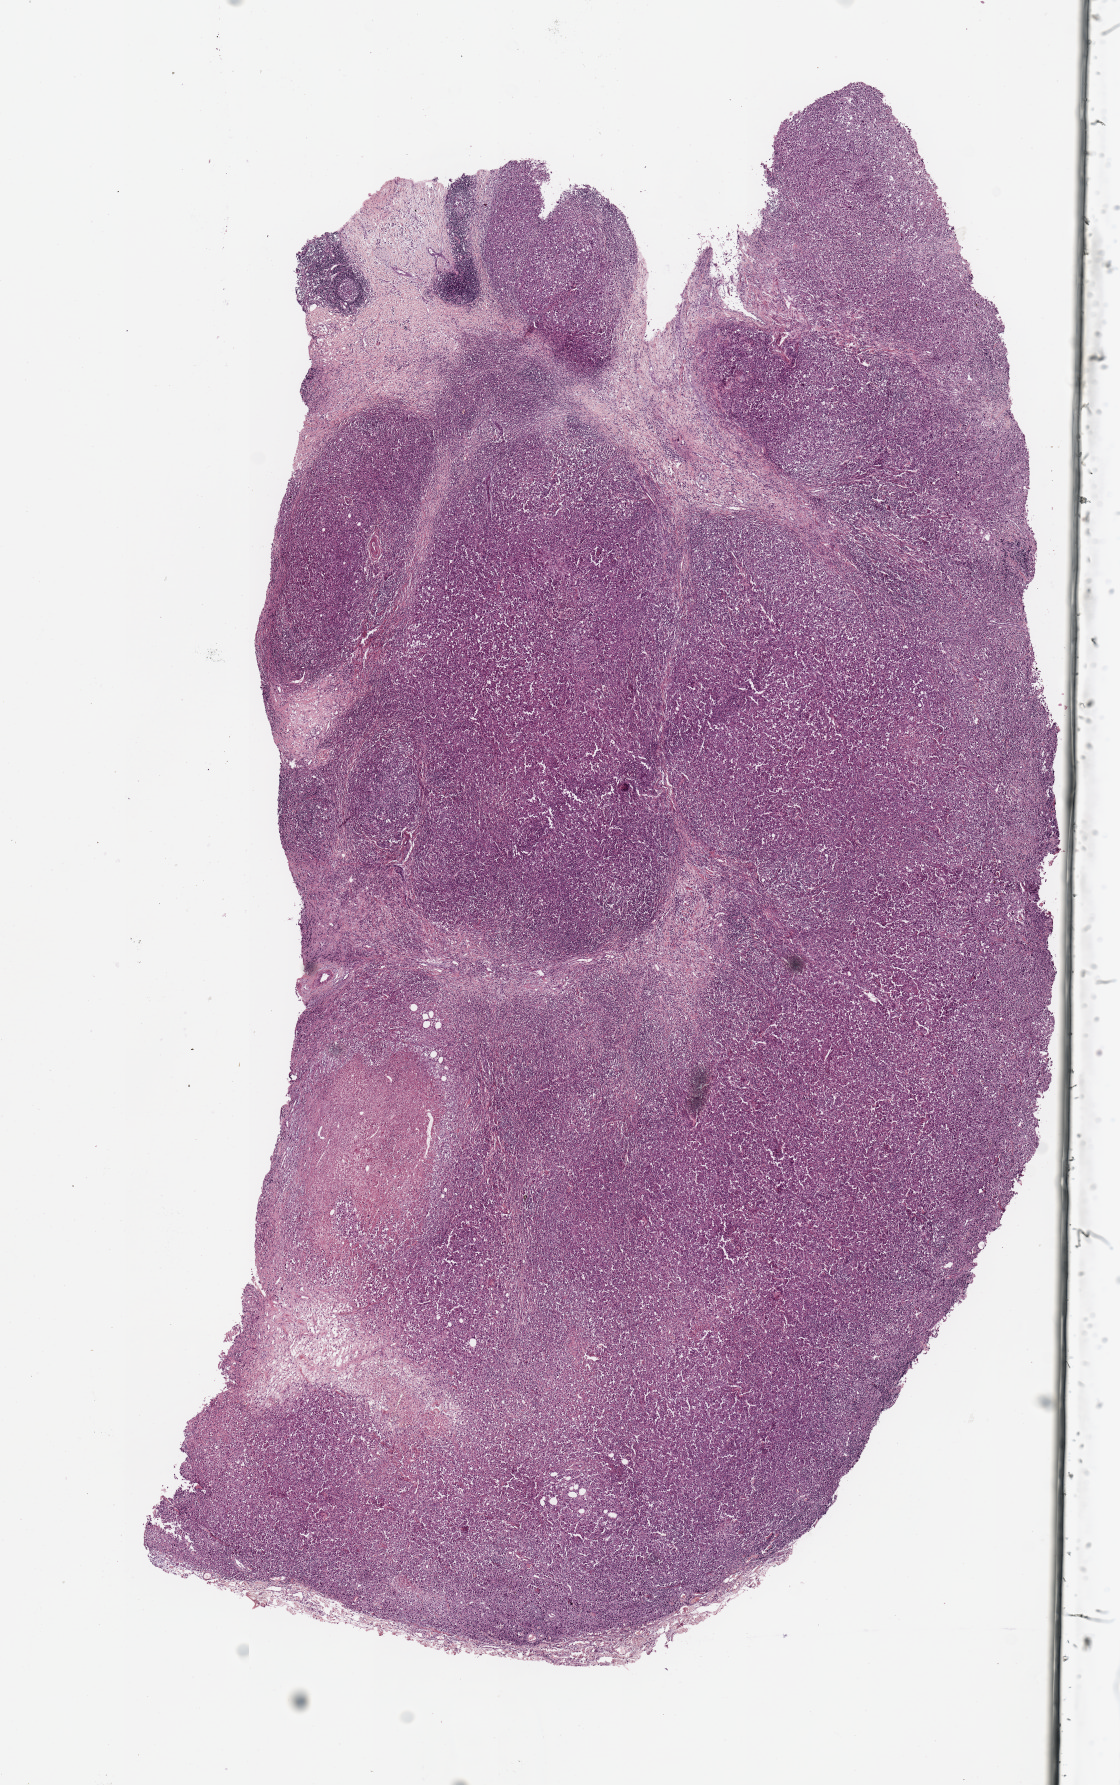
Digitized H&E tissue section (whole slide), shown as a low-resolution overview of the whole scanned area (about 8.9 x 14.1 mm, from a 20x scan). Tumour tissue sample, sampled site: lymph node. Male, 76 y/o. Slide review estimates, as recorded: tumour nuclei 90%, necrosis 0%.
* this section: metastatic tumour tissue
* primary tumour site (as recorded): extremities
* patient diagnosis: Malignant melanoma, NOS